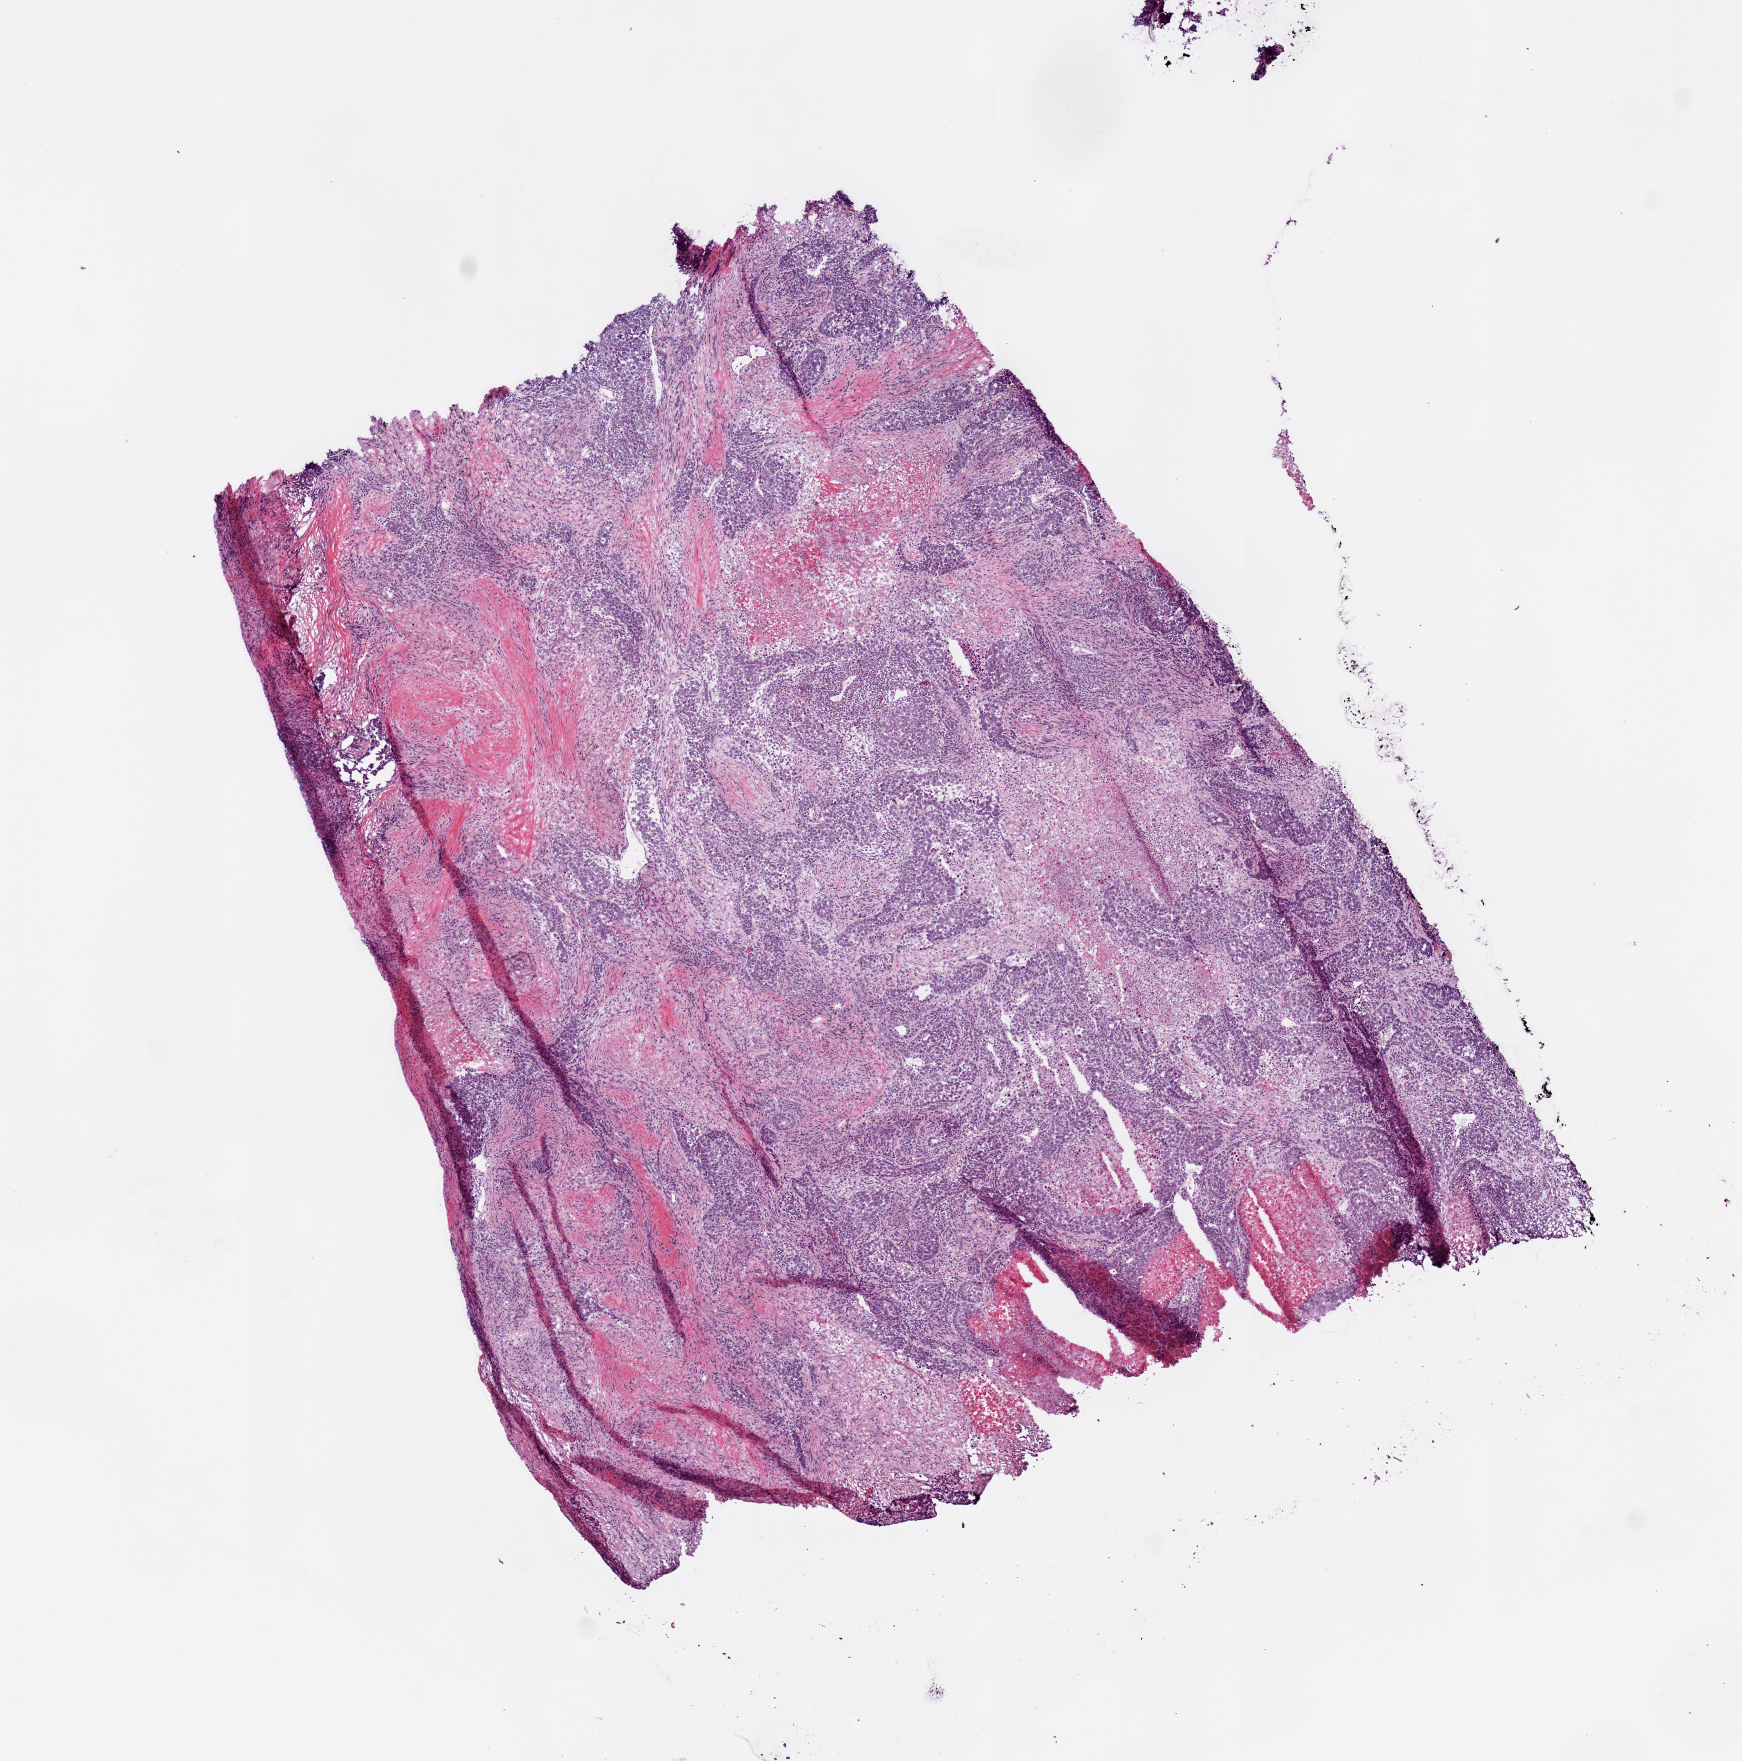
Whole-slide histology image, Hematoxylin and eosin (H&E) stained, a low-resolution overview of the entire scanned area, about 6.9 x 7.0 mm; frozen section from the bottom of the tissue portion; lung, primary tumour sample. Patient: male, age at initial diagnosis 52 years. Pathologist review of this section (percent, as recorded): tumour cells 90%, tumour nuclei 70%, normal cells 0%, stromal cells 0%, necrosis 10%. Inflammatory infiltration, as recorded: lymphocyte infiltration 20%, monocyte infiltration 0%, neutrophil infiltration 5%.
Pathologic diagnosis: Adenocarcinoma, NOS (upper lobe, lung). TNM: T2 N0 M0. AJCC pathologic stage: IB (6th edition). Laterality: left.